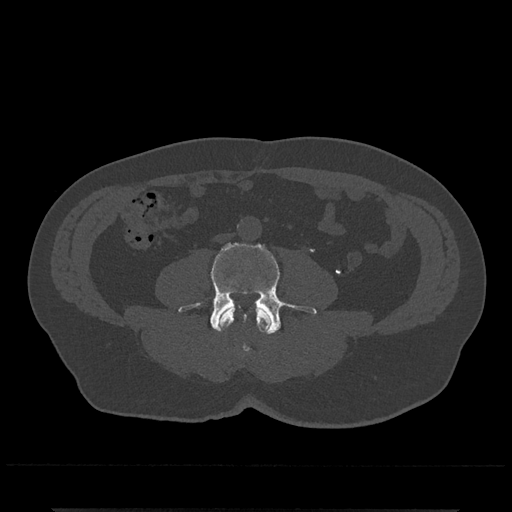
CT including the spine, one axial slice; slice 173 of 797 in the series (ordered by position); 120 kVp; bone window (W 1800 / L 400 HU); 512 × 512 image matrix. Male patient, age 67 years. Case-level facts recorded for this patient, not image findings: primary cancer: prostate.
Structures marked on this image (semi-automatic segmentation, software-assisted and operator-edited):
- L3 vertebra: bounding box [x1, y1, x2, y2] px = [218, 306, 272, 352]
- L4 vertebra: [178, 242, 317, 334]